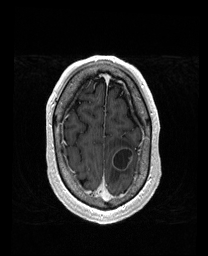
Brain MRI from a brain-tumour surgery series, one axial slice; slice 147 of 192 in the series (ordered by position); T1-weighted post-contrast; 208 × 256 image matrix. From the clinical record (not read from this slice): histopathology: Metastatic Carcinoma from Lung Adenocarcinoma; tumour location: Left Frontal.
Structures marked on this image (manually delineated by an expert):
- tumour: bounding box <113,147,133,171> (left, top, right, bottom; pixels)